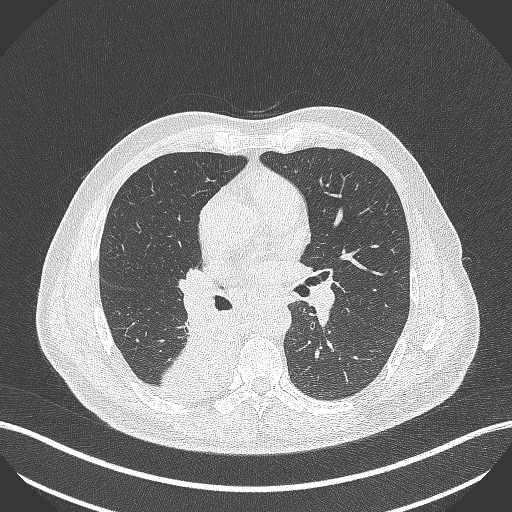
Chest CT, one axial slice. Slice 258 of 451 in the series (ordered by position). Reconstruction kernel B70f. 100 kVp. Lung window (W 1500 / L -600 HU). 1 mm slice thickness. 512 × 512 image matrix. Patient: male, 61 years. From the clinical record (not read from this slice): clinical TNM (as recorded): T1 N0 M0; histopathological grade: G3.
Structures marked on this image (bounding box drawn by a radiologist):
- lung tumour (recorded histology: small cell carcinoma): bounding box [x1, y1, x2, y2] px = [161, 315, 239, 400]